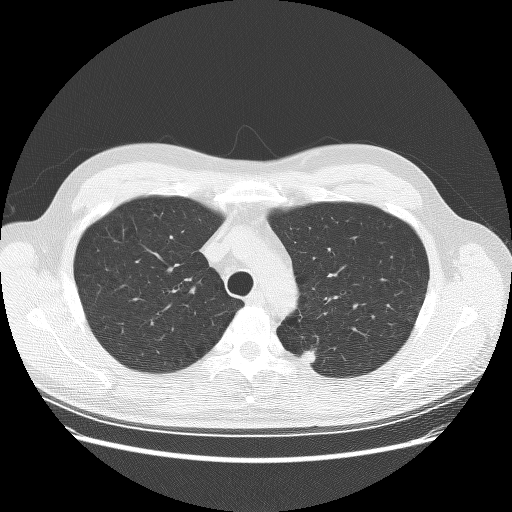
Low-dose screening chest CT, one axial slice; slice 203 of 253 in the series (ordered by position); 120 kVp; lung window (W 1500 / L -600 HU); 2.5 mm slice thickness; 512 × 512 image matrix, field of view 370 × 370 mm.
Annotated regions visible in this slice (expert manual segmentation):
- lesion 2 (nodule): bounding box (x1, y1, x2, y2) in pixels: (301, 350, 318, 363)